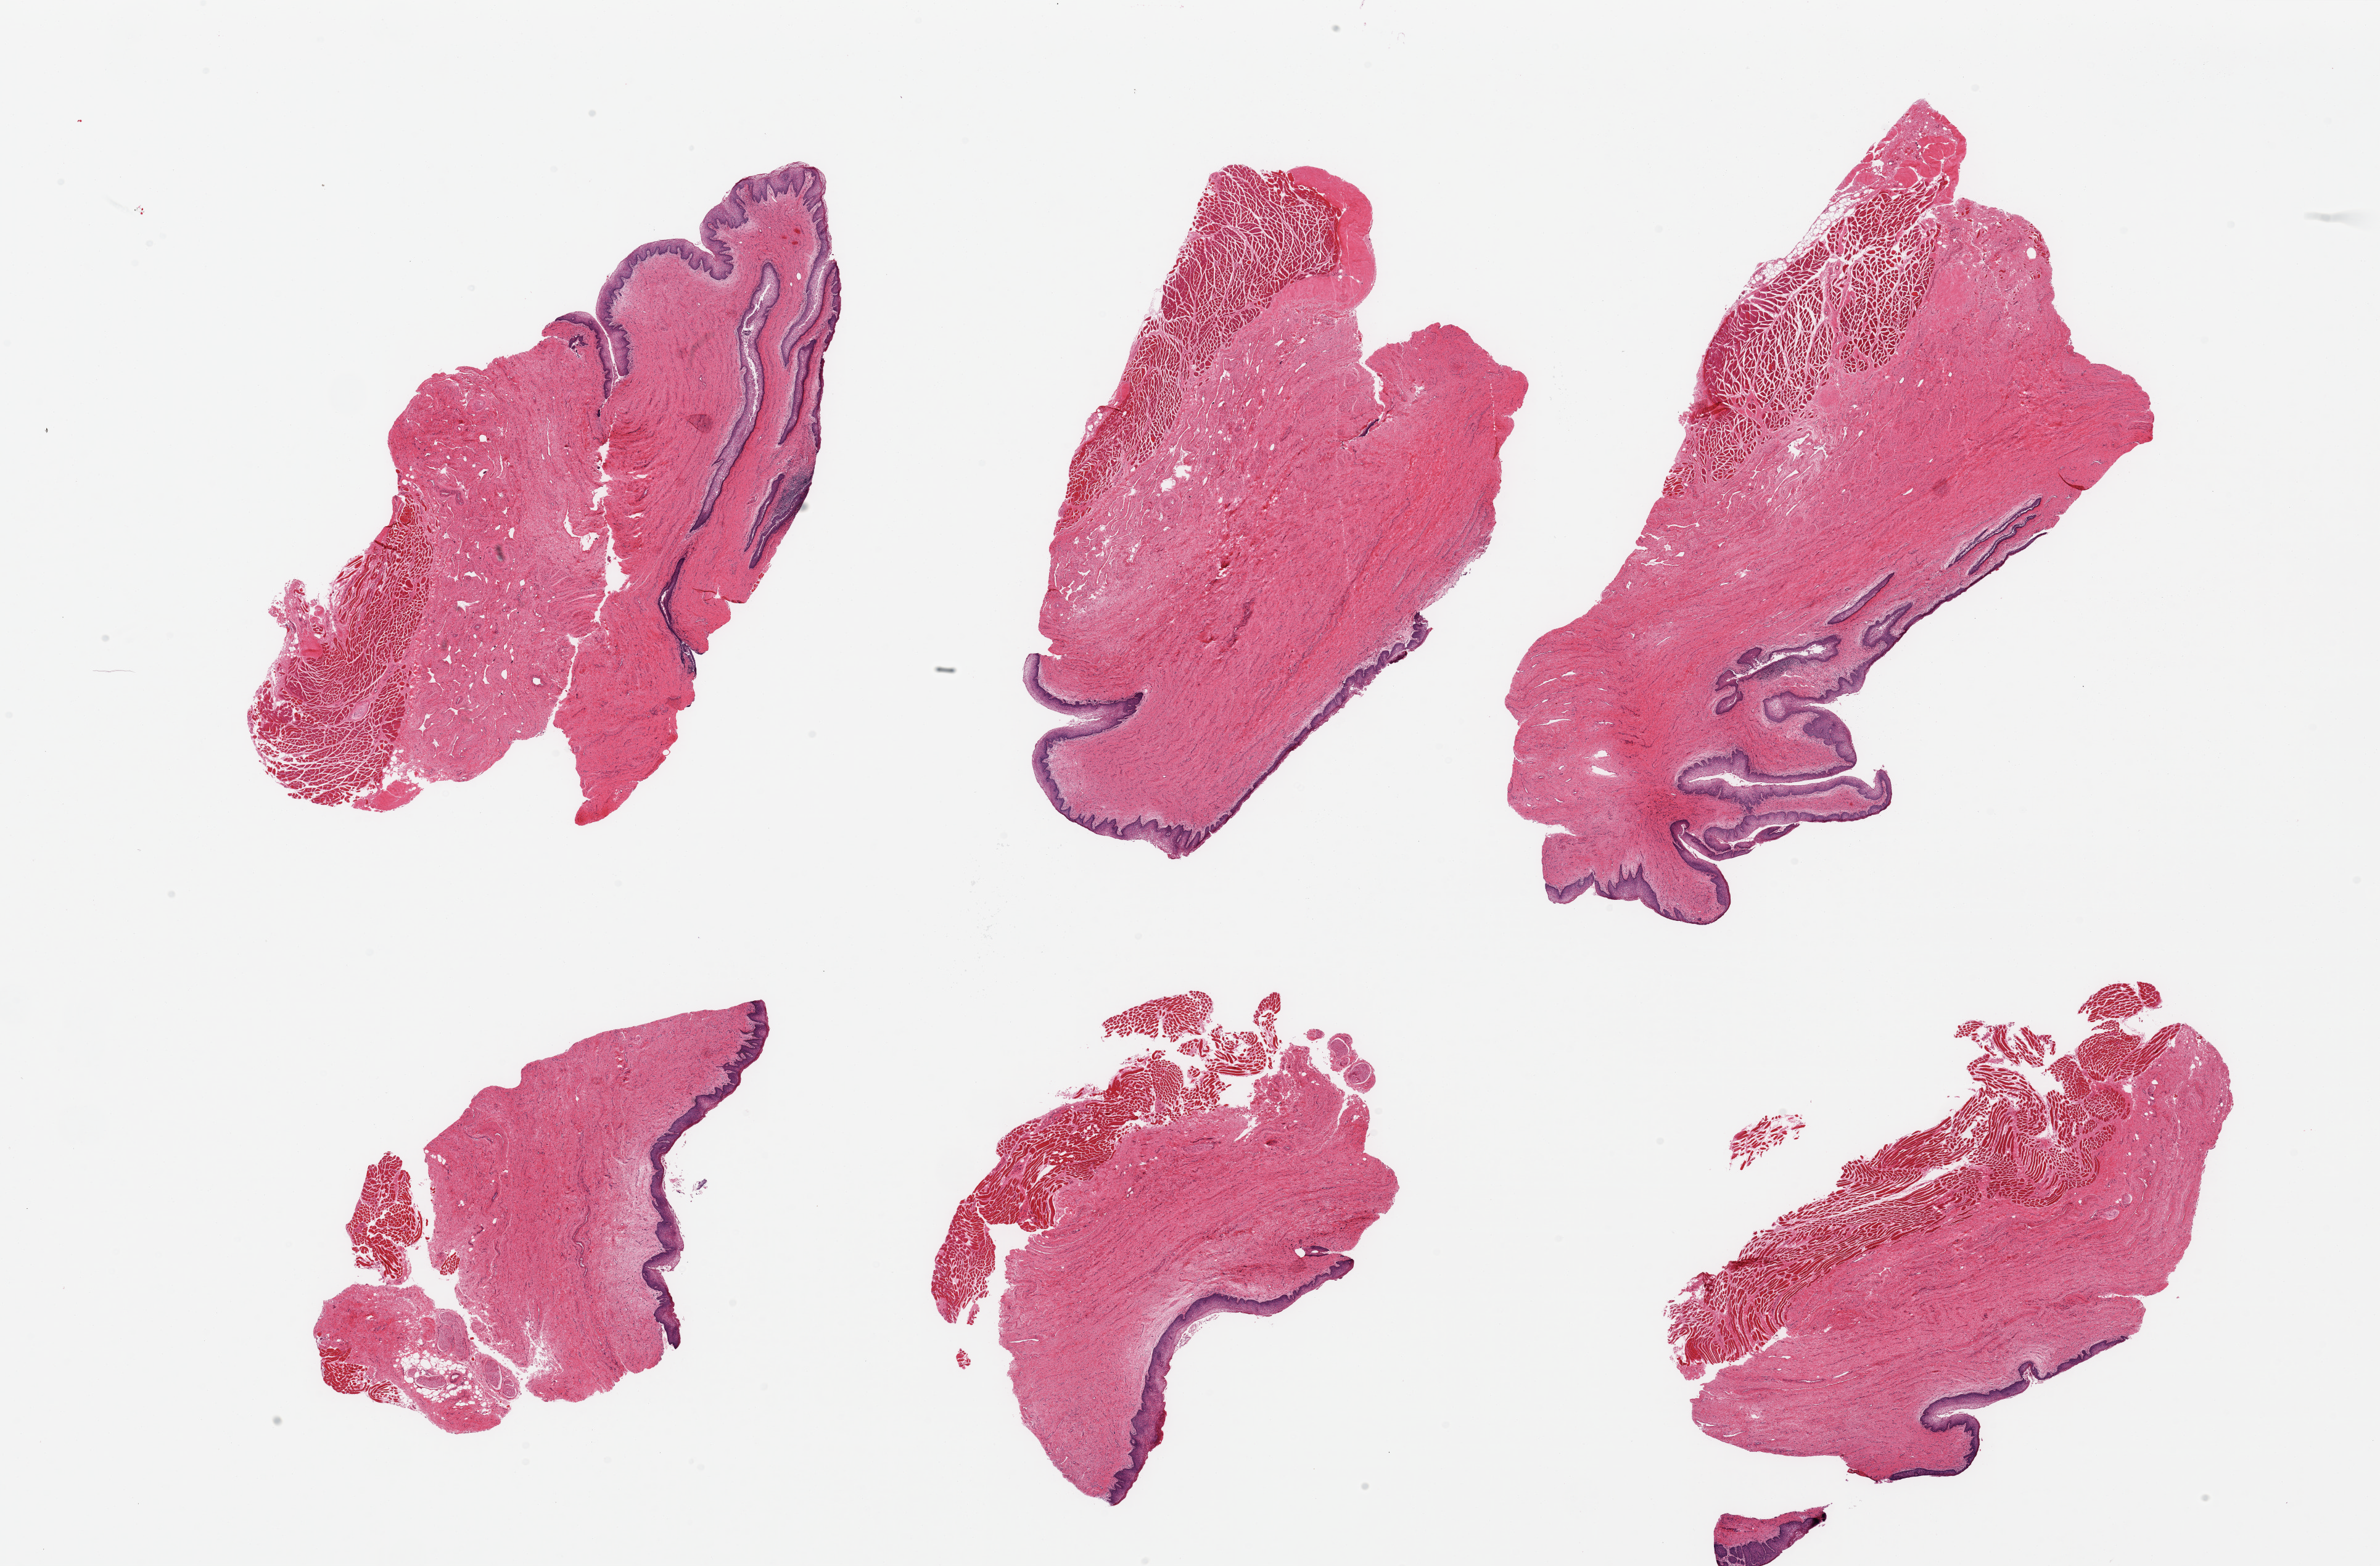
Whole-slide image, haematoxylin and eosin stain, low-resolution overview of the scanned area, about 30.5 x 20.1 mm, PAXgene-fixed, paraffin-embedded tissue, sampled site (target tissue): vagina, donor tissue sample. Female donor.
* review note (as recorded): 6 pieces; papillary surface on some pieces